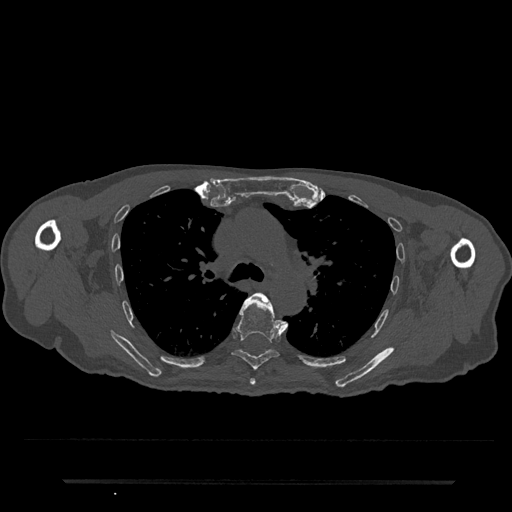
CT including the spine, one axial slice; slice 535 of 797 in the series (ordered by position); bone window (W 1800 / L 400 HU); 0.5 mm slice thickness; 512 × 512 image matrix. Male patient, age 74 years. Case-level facts recorded for this patient, not image findings: primary cancer: prostate.
Annotated regions visible in this slice (semi-automatic segmentation, software-assisted and operator-edited):
- T5 vertebra: bounding box (x1, y1, x2, y2) in pixels: (250, 298, 288, 385)
- T6 vertebra: (232, 292, 281, 370)